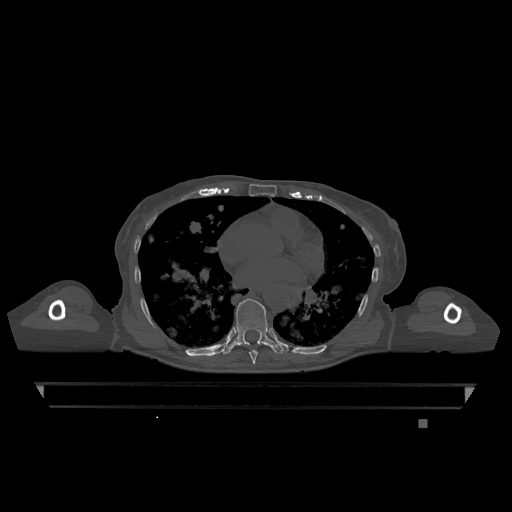
CT including the spine, one axial slice; position 707 of 1317 along the scan axis; bone window (W 1800 / L 400 HU); 512 × 512 image matrix, field of view 500 × 500 mm. Patient: female, 74 years. Case-level facts recorded for this patient, not image findings: primary cancer: lung.
Annotated regions visible in this slice (semi-automatic segmentation, software-assisted and operator-edited):
- T7 vertebra: box from (x=249, y=350) to (x=258, y=364) px
- T9 vertebra: (x=222, y=299)–(x=283, y=355)